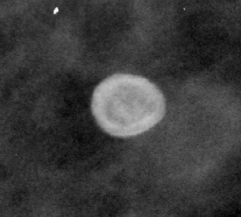
Cropped region of a digitized screen-film mammogram centred on a radiologist-marked abnormality, left breast, CC view, BI-RADS breast density category 3 (scale 1–4).
Marked abnormality: calcifications, morphology round and regular / eggshell; BI-RADS assessment category 2; subtlety rating 3 on a 1 (subtle) to 5 (obvious) scale; benign; no additional work-up was recommended (benign without callback).